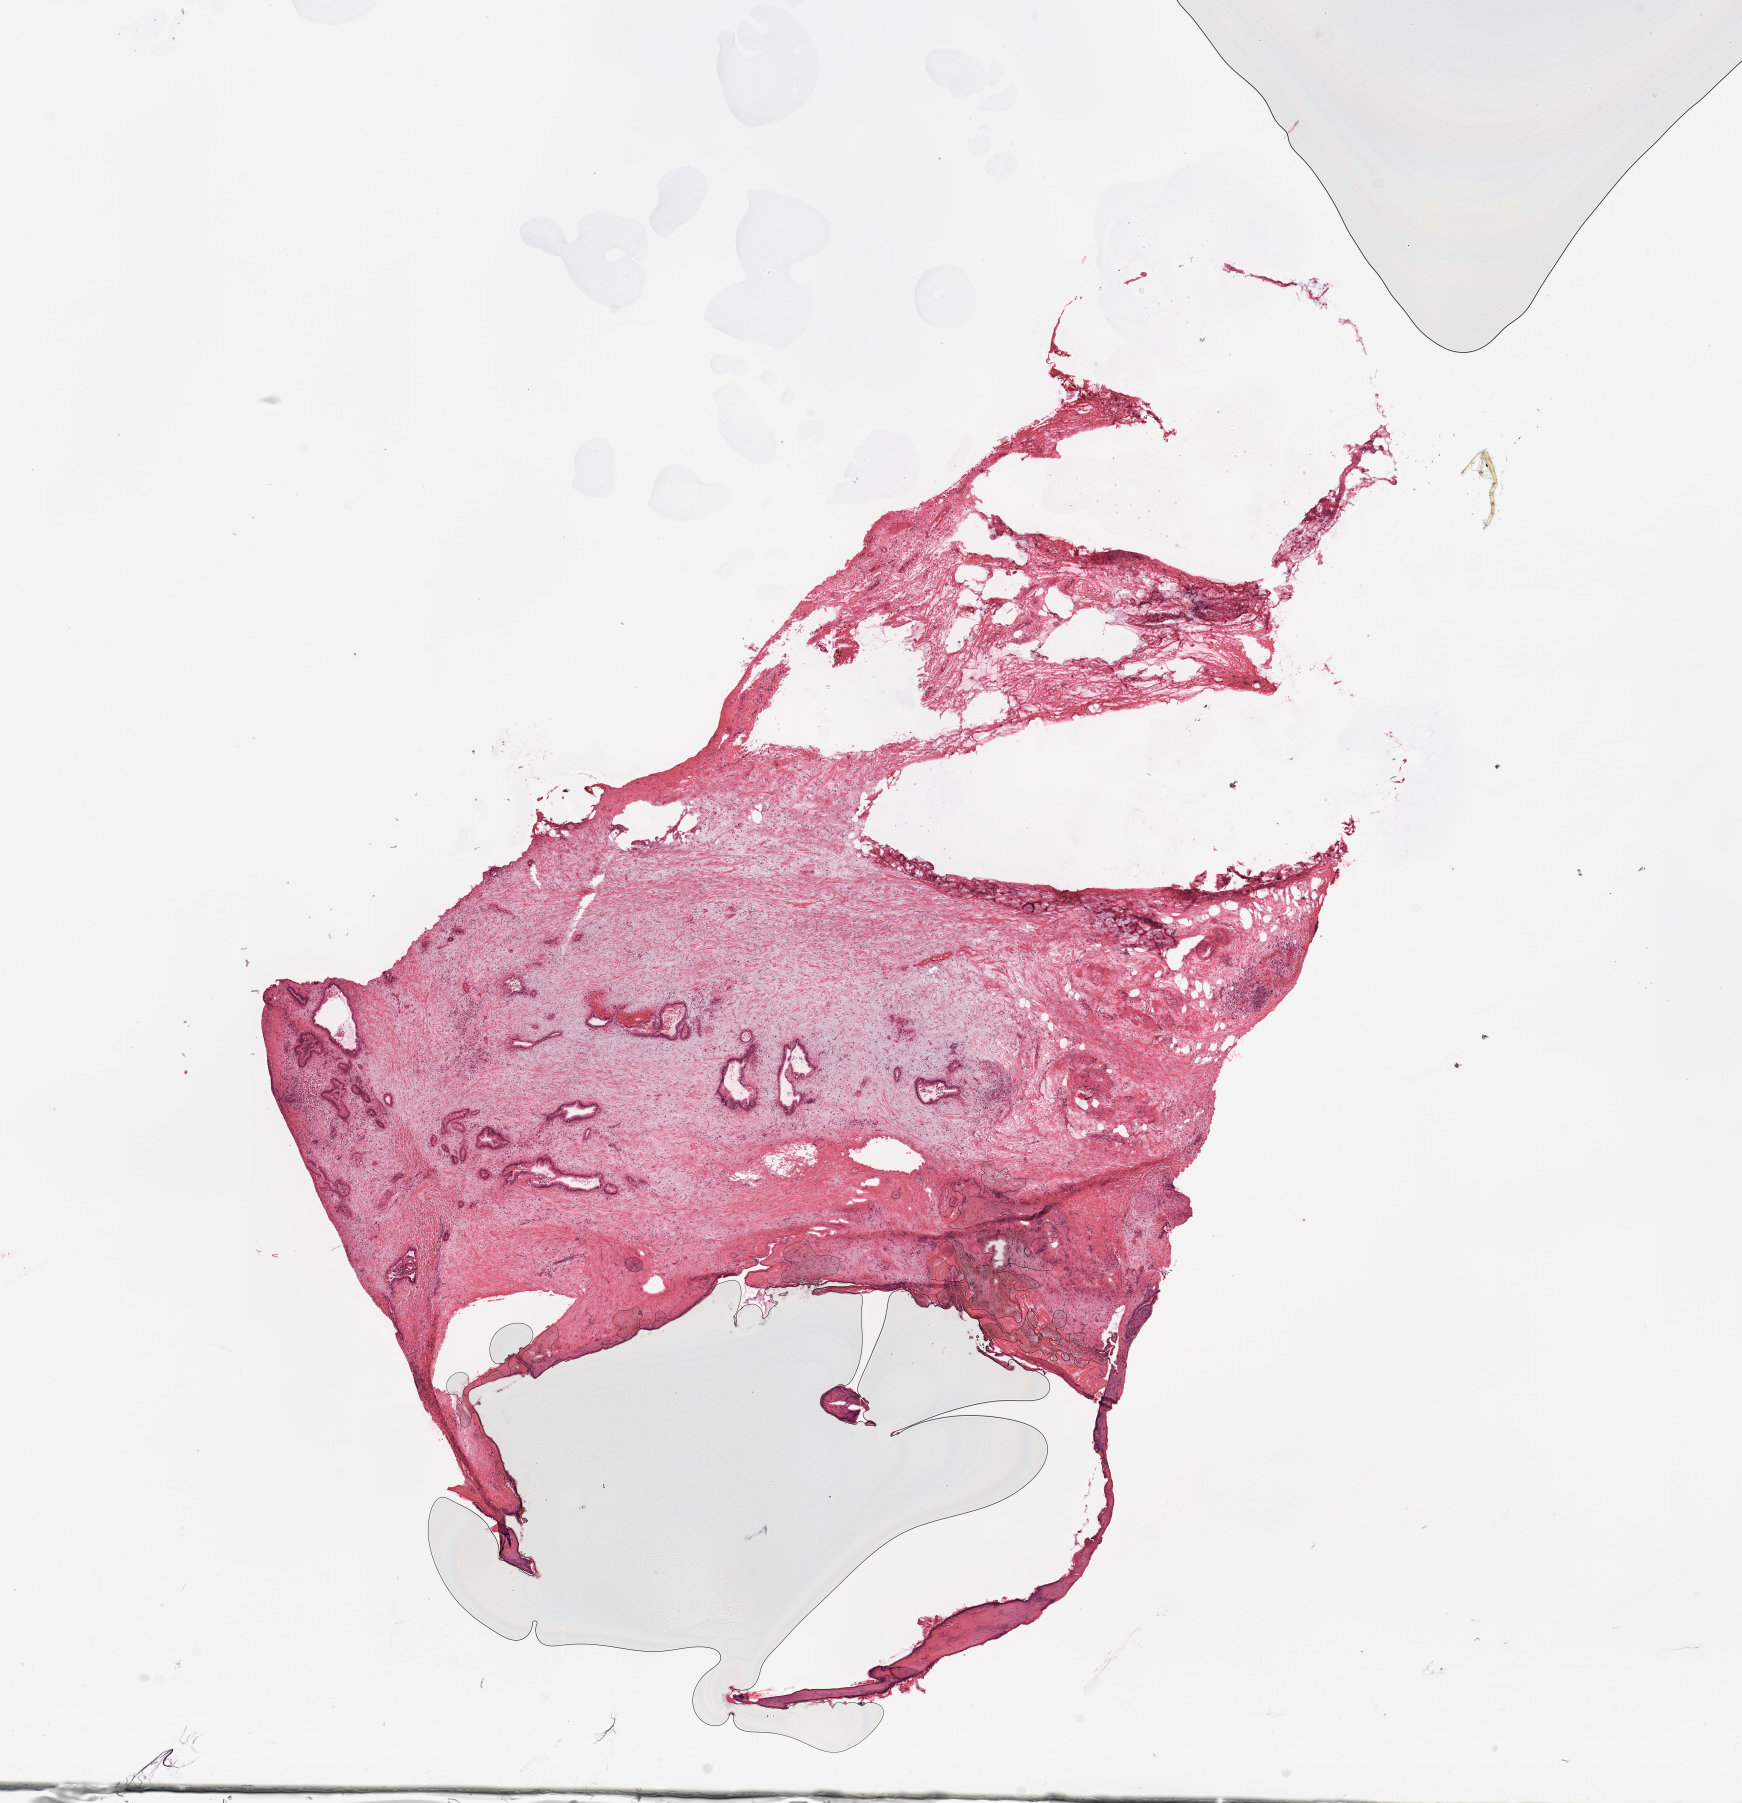
Digitized Hematoxylin and eosin (H&E) stained tissue section (whole slide), low-resolution overview of the scanned area, about 13.8 x 14.3 mm; tumour tissue sample, sampled site: pancreas. 62-year-old male patient. Histologic grade: G1 (well differentiated). Slide review estimates, as recorded: tumour nuclei 10%, necrosis 0%.
Histologic diagnosis: Infiltrating duct carcinoma, NOS. AJCC pathologic stage: IIB.